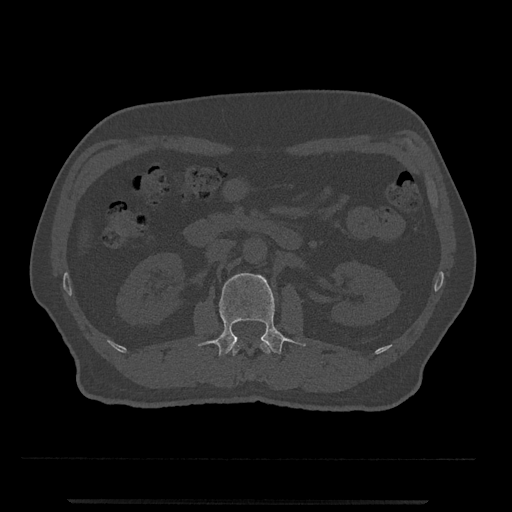
CT including the spine, one axial slice; reconstruction kernel Br40s/3; bone window (W 1800 / L 400 HU); 0.5 mm slice thickness; 512 × 512 image matrix, field of view 419 × 419 mm. Male patient, age 63 years. Case-level facts recorded for this patient, not image findings: primary cancer: prostate.
Outlined on this slice (semi-automatic segmentation, software-assisted and operator-edited):
- L1 vertebra: box from (x=231, y=341) to (x=272, y=356) px
- L2 vertebra: (x=197, y=273)–(x=306, y=357)